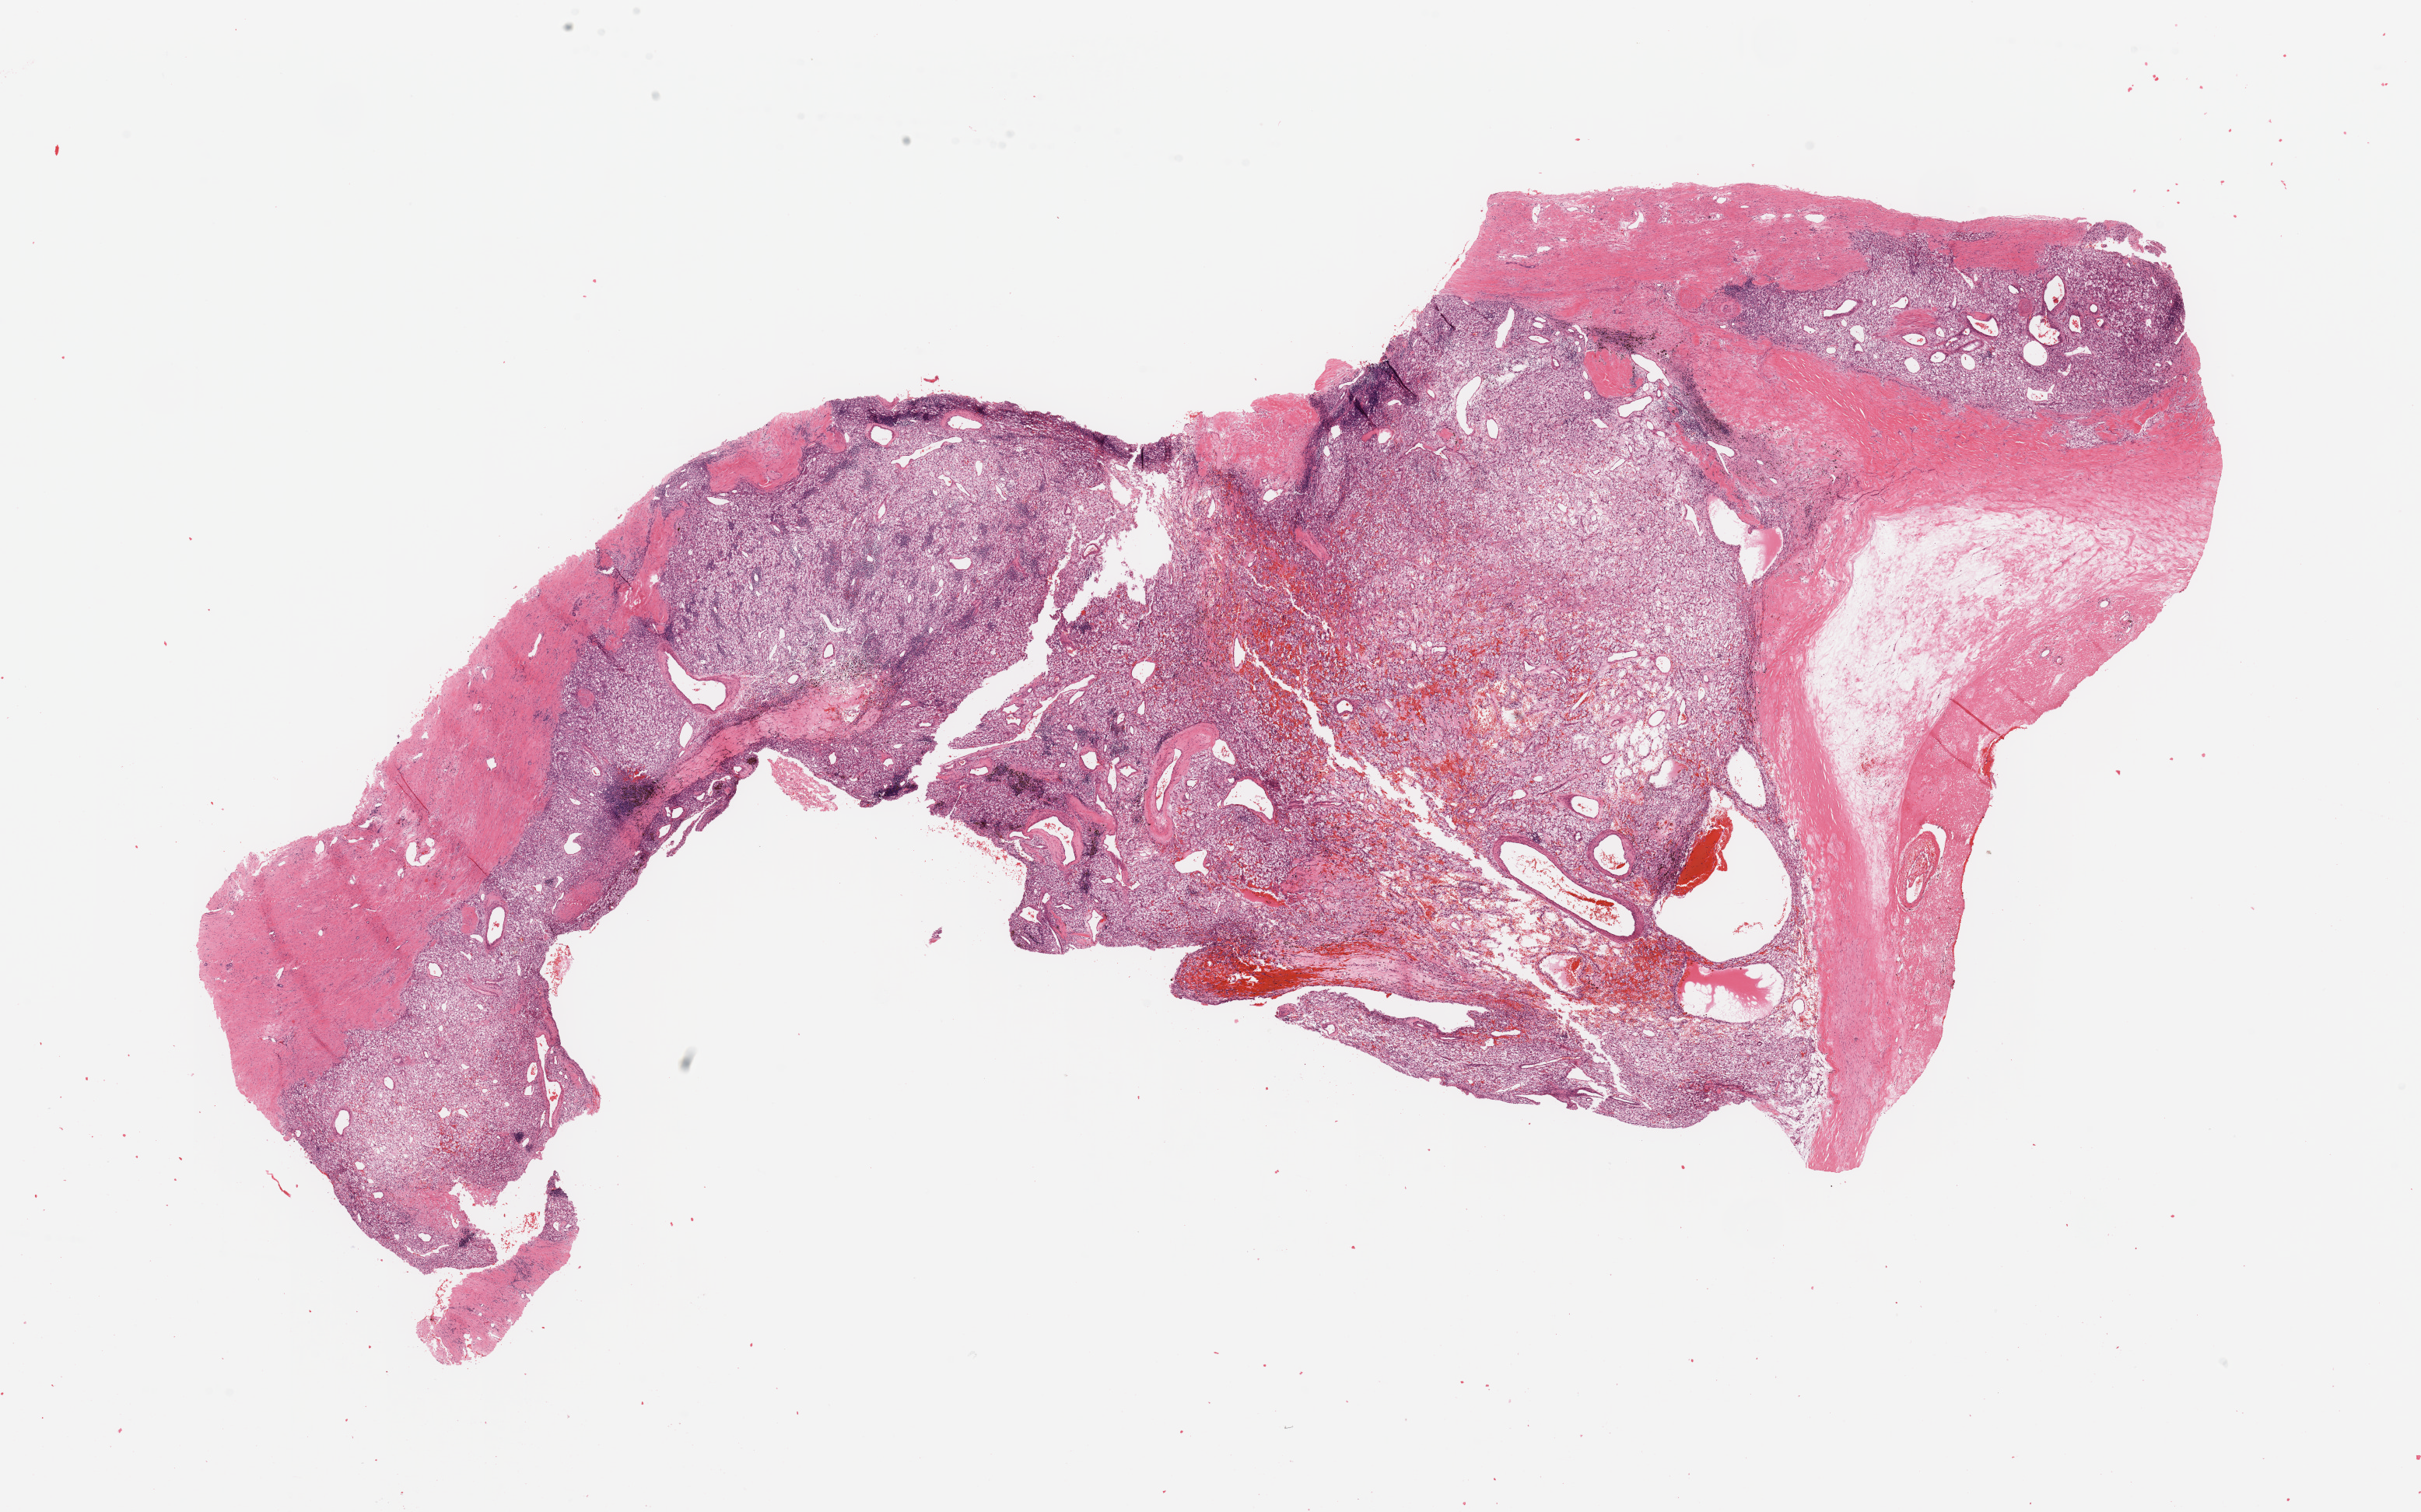
Whole-slide histology image, H&E-stained — shown as a low-resolution overview of the whole scanned area (about 24.6 x 15.4 mm, acquisition: 20x scan). Tumour tissue sample, kidney. 61-year-old male patient. Histologic grade: G2 (moderately differentiated).
- histologic diagnosis: Renal cell carcinoma, NOS